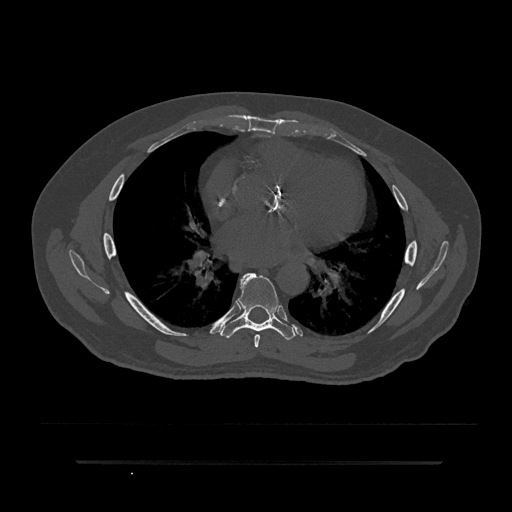
CT including the spine, one axial slice; bone window (W 1800 / L 400 HU); 0.5 mm slice thickness; 512 × 512 image matrix, field of view 464 × 464 mm. Male patient, age 59 years. From the clinical record (not read from this slice): primary cancer: bile ducts; vertebrae with lytic lesions (as recorded): T10.
Structures marked on this image (semi-automatically segmented with operator editing):
- T6 vertebra: bounding box (x1, y1, x2, y2) in pixels: (254, 334, 260, 348)
- T7 vertebra: (220, 273, 296, 340)